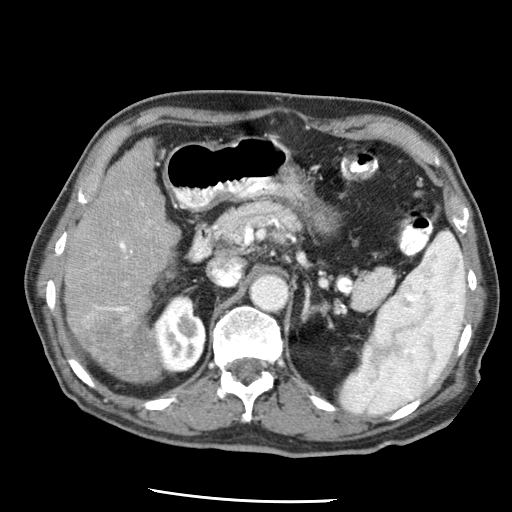
Contrast-enhanced abdominal CT (liver protocol), one axial slice; position 25 of 79 along the scan axis; 120 kVp; soft-tissue window (W 400 / L 40 HU); 512 × 512 image matrix. Case-level facts recorded for this patient, not image findings: diagnosis: hepatocellular carcinoma (patient treated with transarterial chemoembolisation; whether this scan precedes or follows treatment is not stated here); TNM stage (as recorded): Stage-IIIA; Child-Pugh class: A; tumour size: 7 cm.
Outlined on this slice (semi-automatically segmented with operator editing):
- liver parenchyma outside the tumour (the mass and vessels are separate outlines, so this box may not span the whole liver): bounding box (x1, y1, x2, y2) in pixels: (62, 139, 178, 380)
- liver vessels: (84, 191, 151, 328)